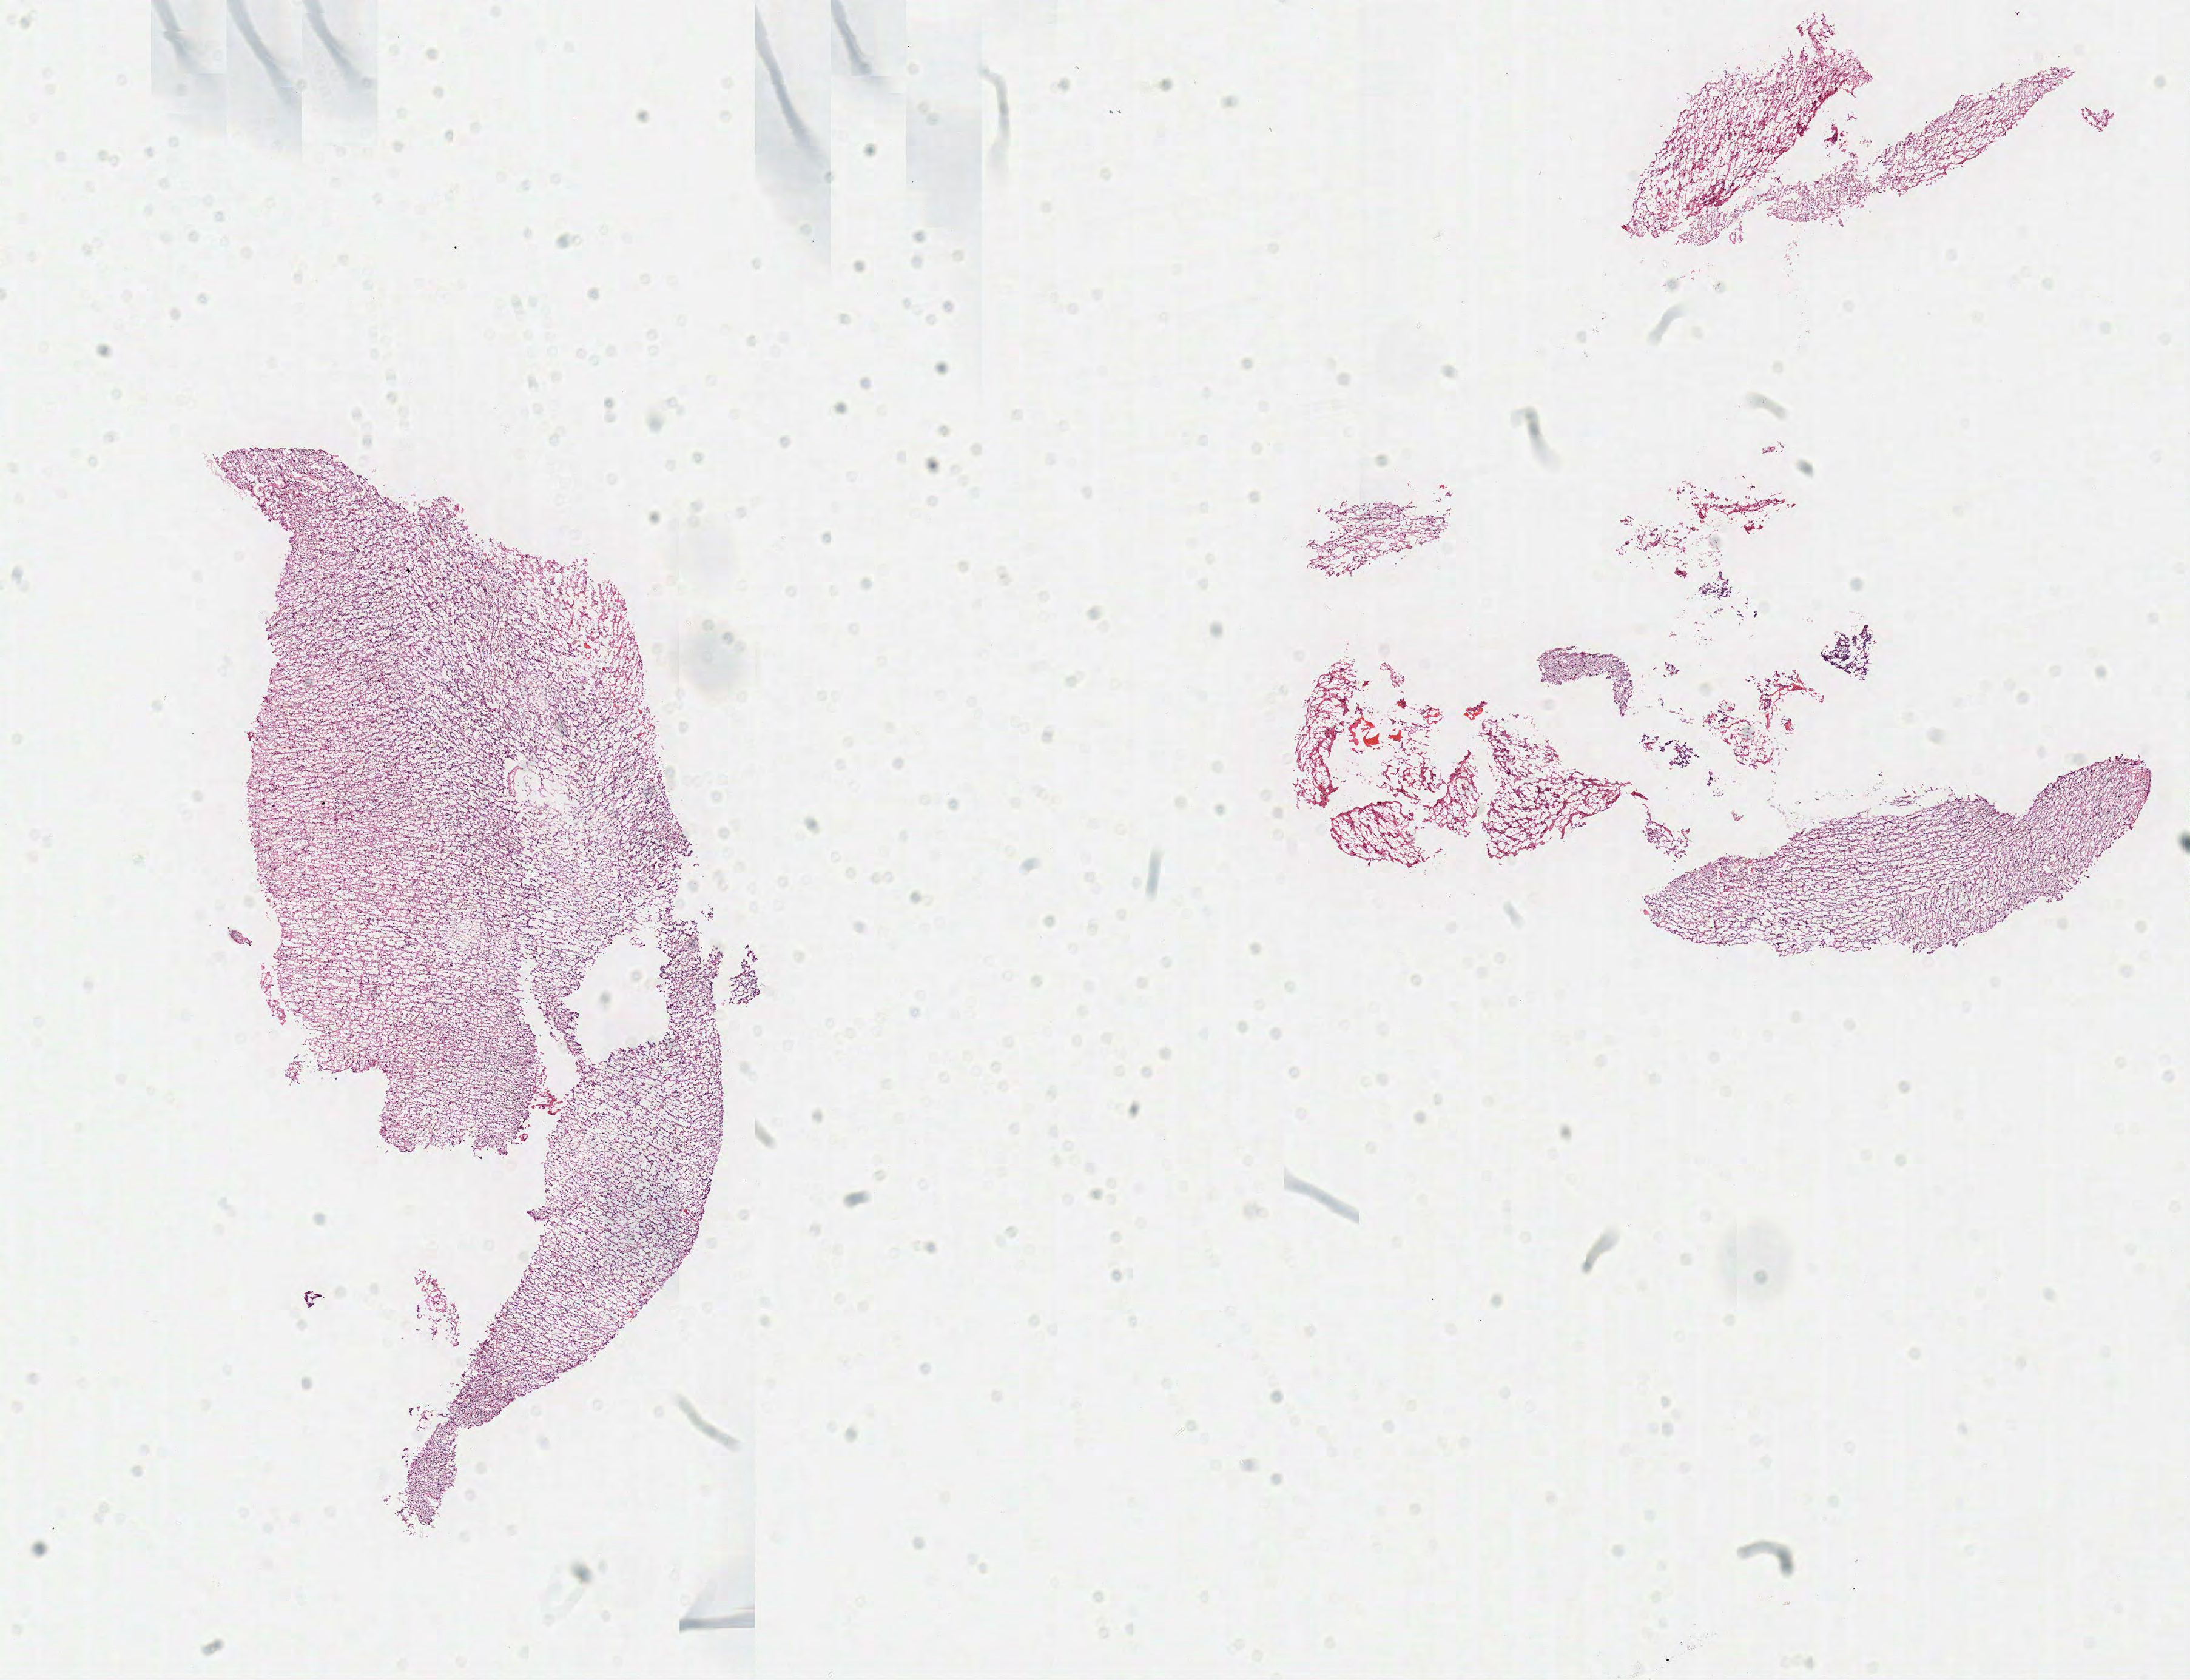
H&E whole-slide image, shown as a low-resolution overview of the whole scanned area (about 14.2 x 10.9 mm, slide scanned at 40x); frozen section from the top of the tissue portion; sample: primary tumour, brain. Patient: female, age at initial diagnosis 72 years. Slide review estimates, as recorded: tumour cells 100%, tumour nuclei 75%, normal cells 0%, stromal cells 0%, necrosis 0%.
• pathologic diagnosis: Glioblastoma